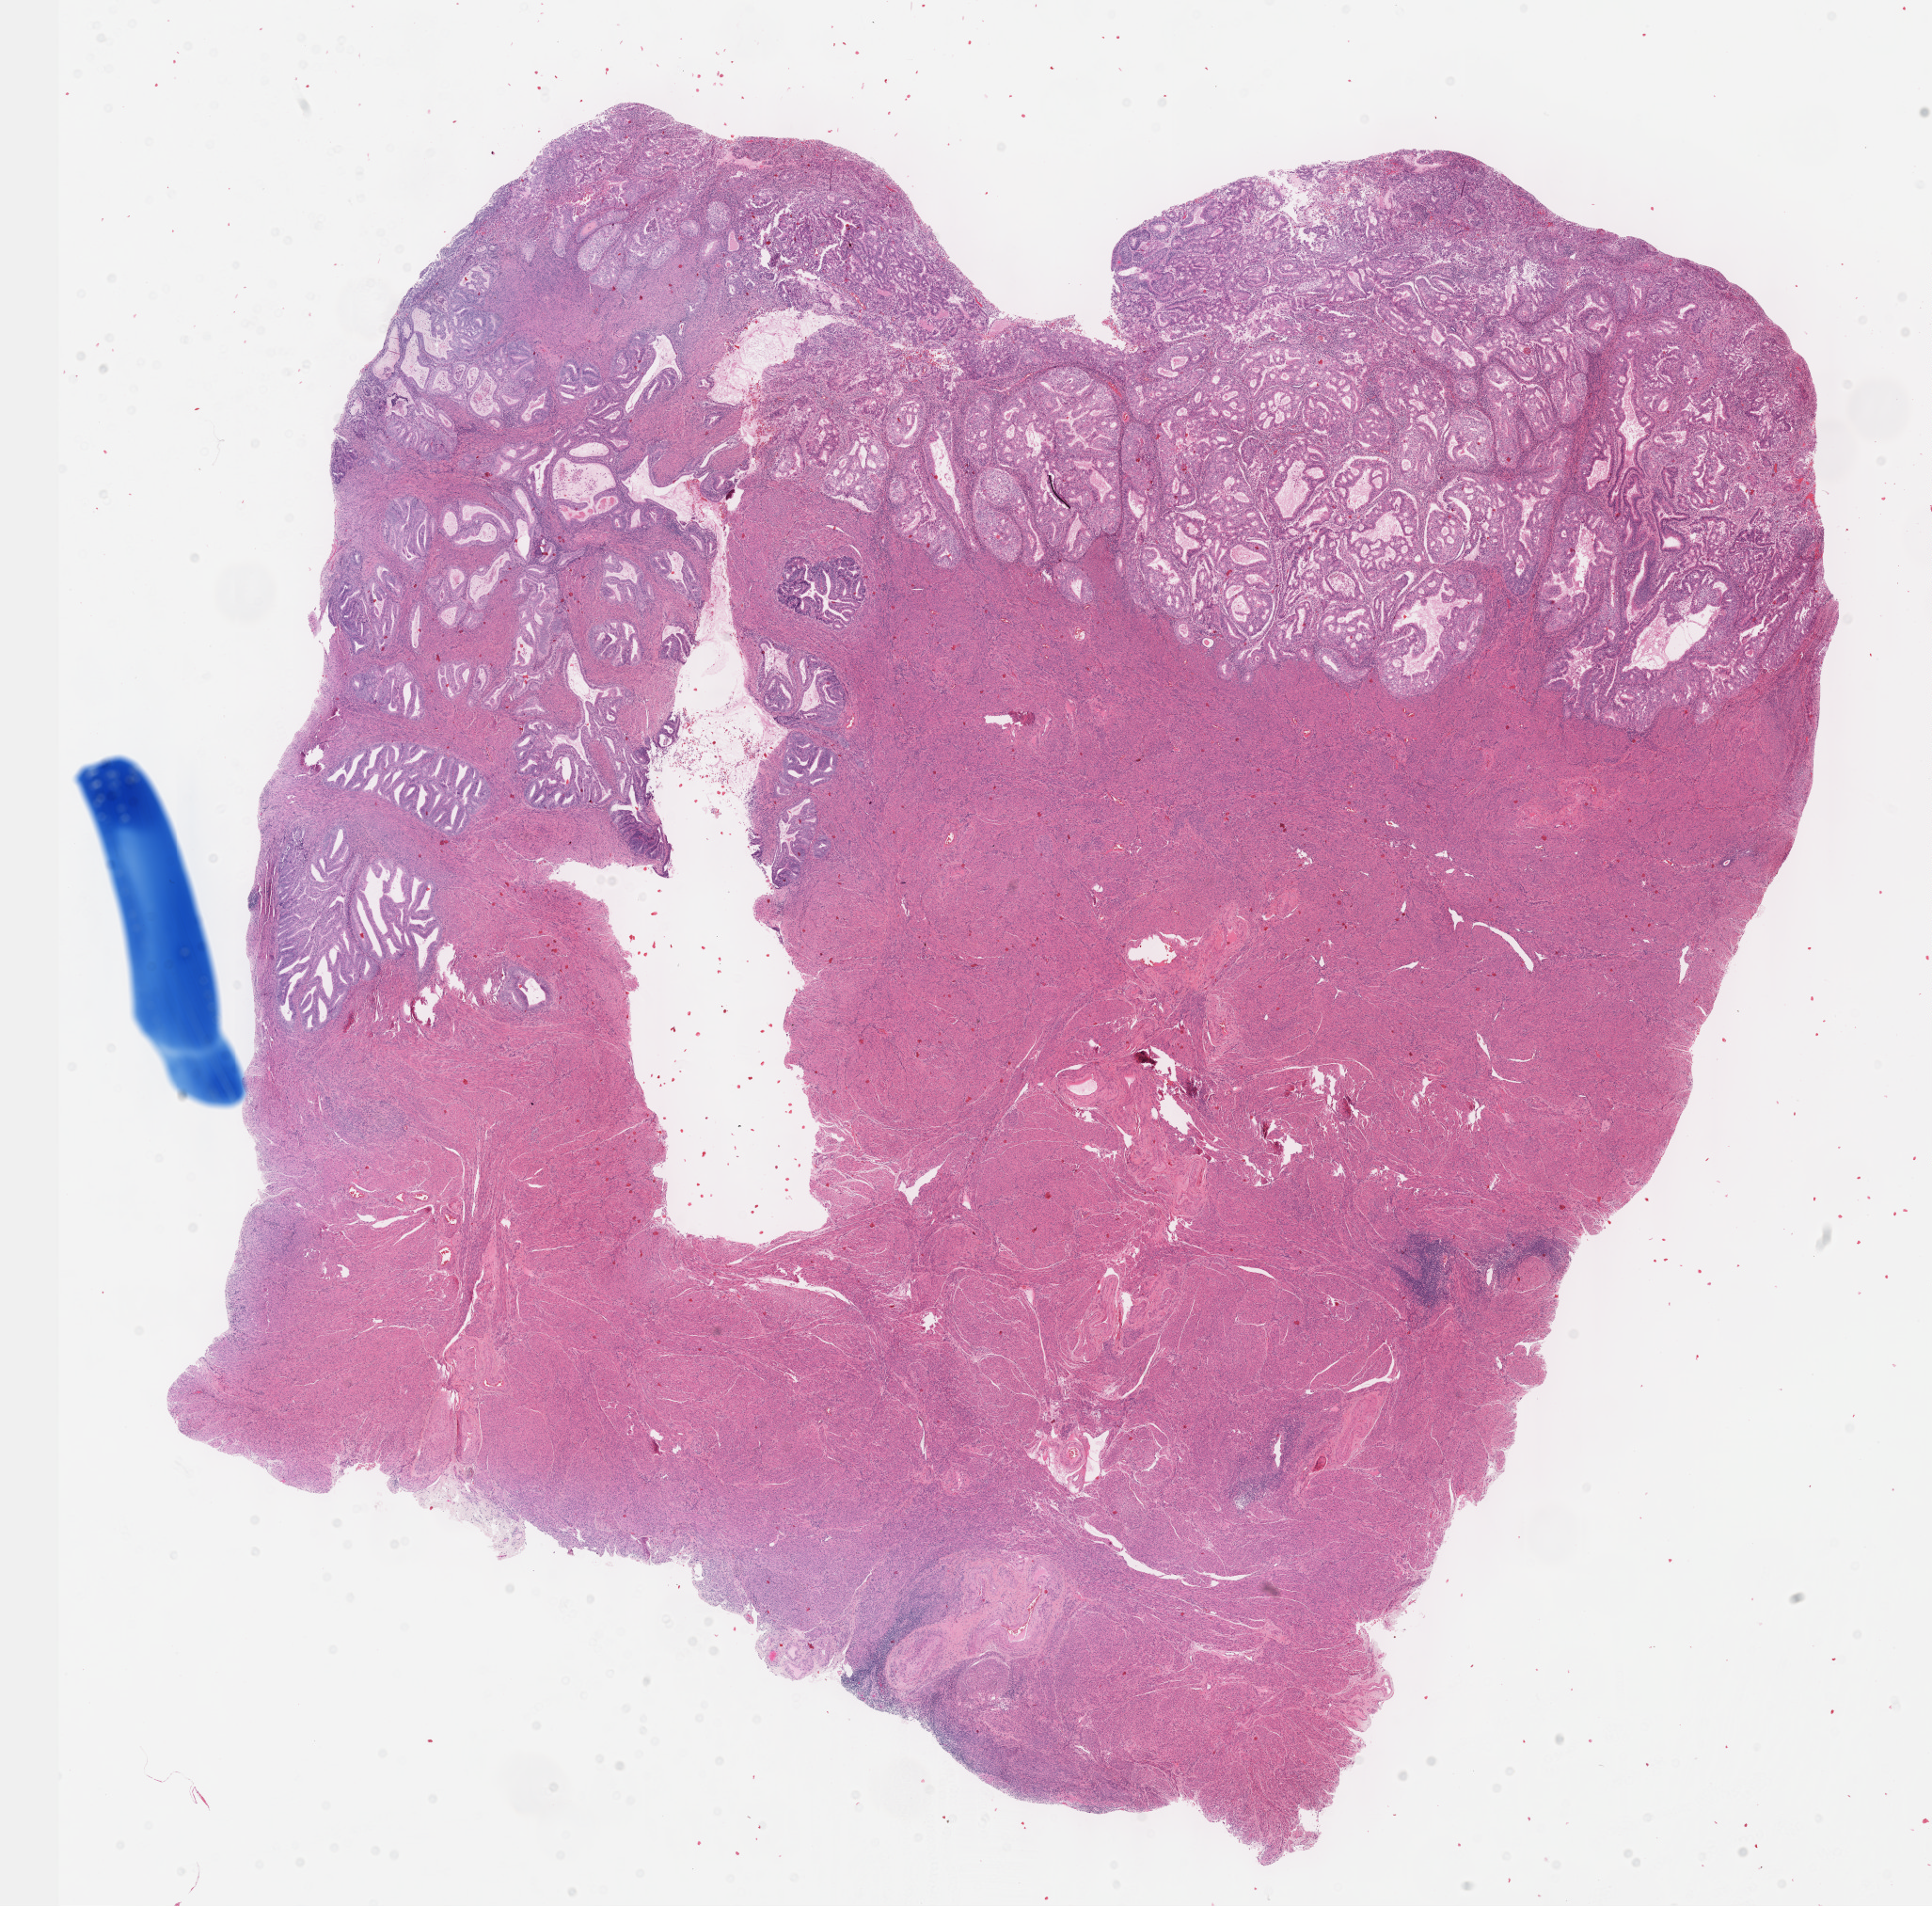
Digitized H&E tissue section (whole slide) — low-resolution overview of the scanned area, about 16.6 x 16.4 mm (from a 40x scan). Formalin-fixed paraffin-embedded (FFPE) diagnostic section. Sample: primary tumour, uterus. Female patient; age at initial diagnosis 70 years. Histologic grade: G2 (moderately differentiated).
- diagnosis: Endometrioid adenocarcinoma, NOS
- FIGO stage: I